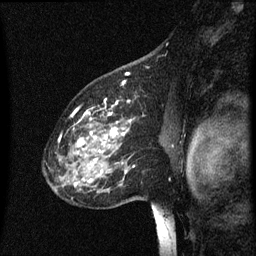
Breast MRI (dynamic contrast-enhanced), one sagittal slice; position 43 of 60 along the scan axis; dynamic contrast-enhanced series, image 2 of 3 at this slice position (ordered by acquisition); 1.5 T; TE 4.2 ms, TR 8 ms; 256 × 256 image matrix, field of view 200 × 200 mm. Female patient, age 60 years.
Structures marked on this image (semi-automatic segmentation, software-assisted and operator-edited):
- analysis volume of interest (the breast-tissue region the enhancement analysis was run in; not a lesion): bounding box (x1, y1, x2, y2) in pixels: (49, 100, 146, 195)
- tumour enhancement mask (voxels above the 70 % enhancement threshold inside the analysis volume of interest): (75, 100, 136, 187)